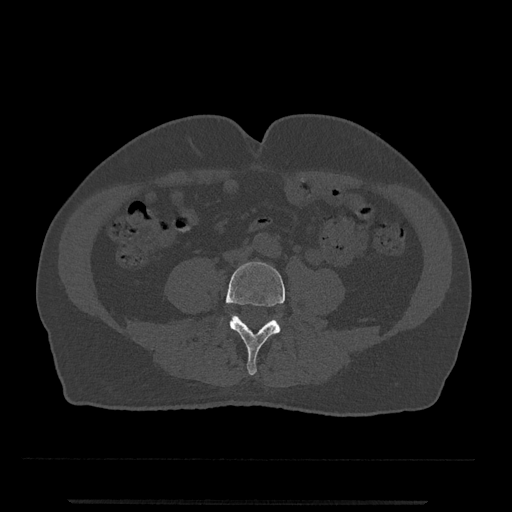
CT including the spine, one axial slice. Position 128 of 797 along the scan axis. Reconstruction kernel Br40s/3. Bone window (W 1800 / L 400 HU). 0.5 mm slice thickness. 512 × 512 image matrix, field of view 419 × 419 mm. Patient: male, 63 years. Case-level facts recorded for this patient, not image findings: primary cancer: prostate.
Annotated regions visible in this slice (semi-automatic segmentation, software-assisted and operator-edited):
- L4 vertebra: bounding box (x1, y1, x2, y2) in pixels: (225, 261, 285, 375)
- L5 vertebra: (278, 324, 280, 327)